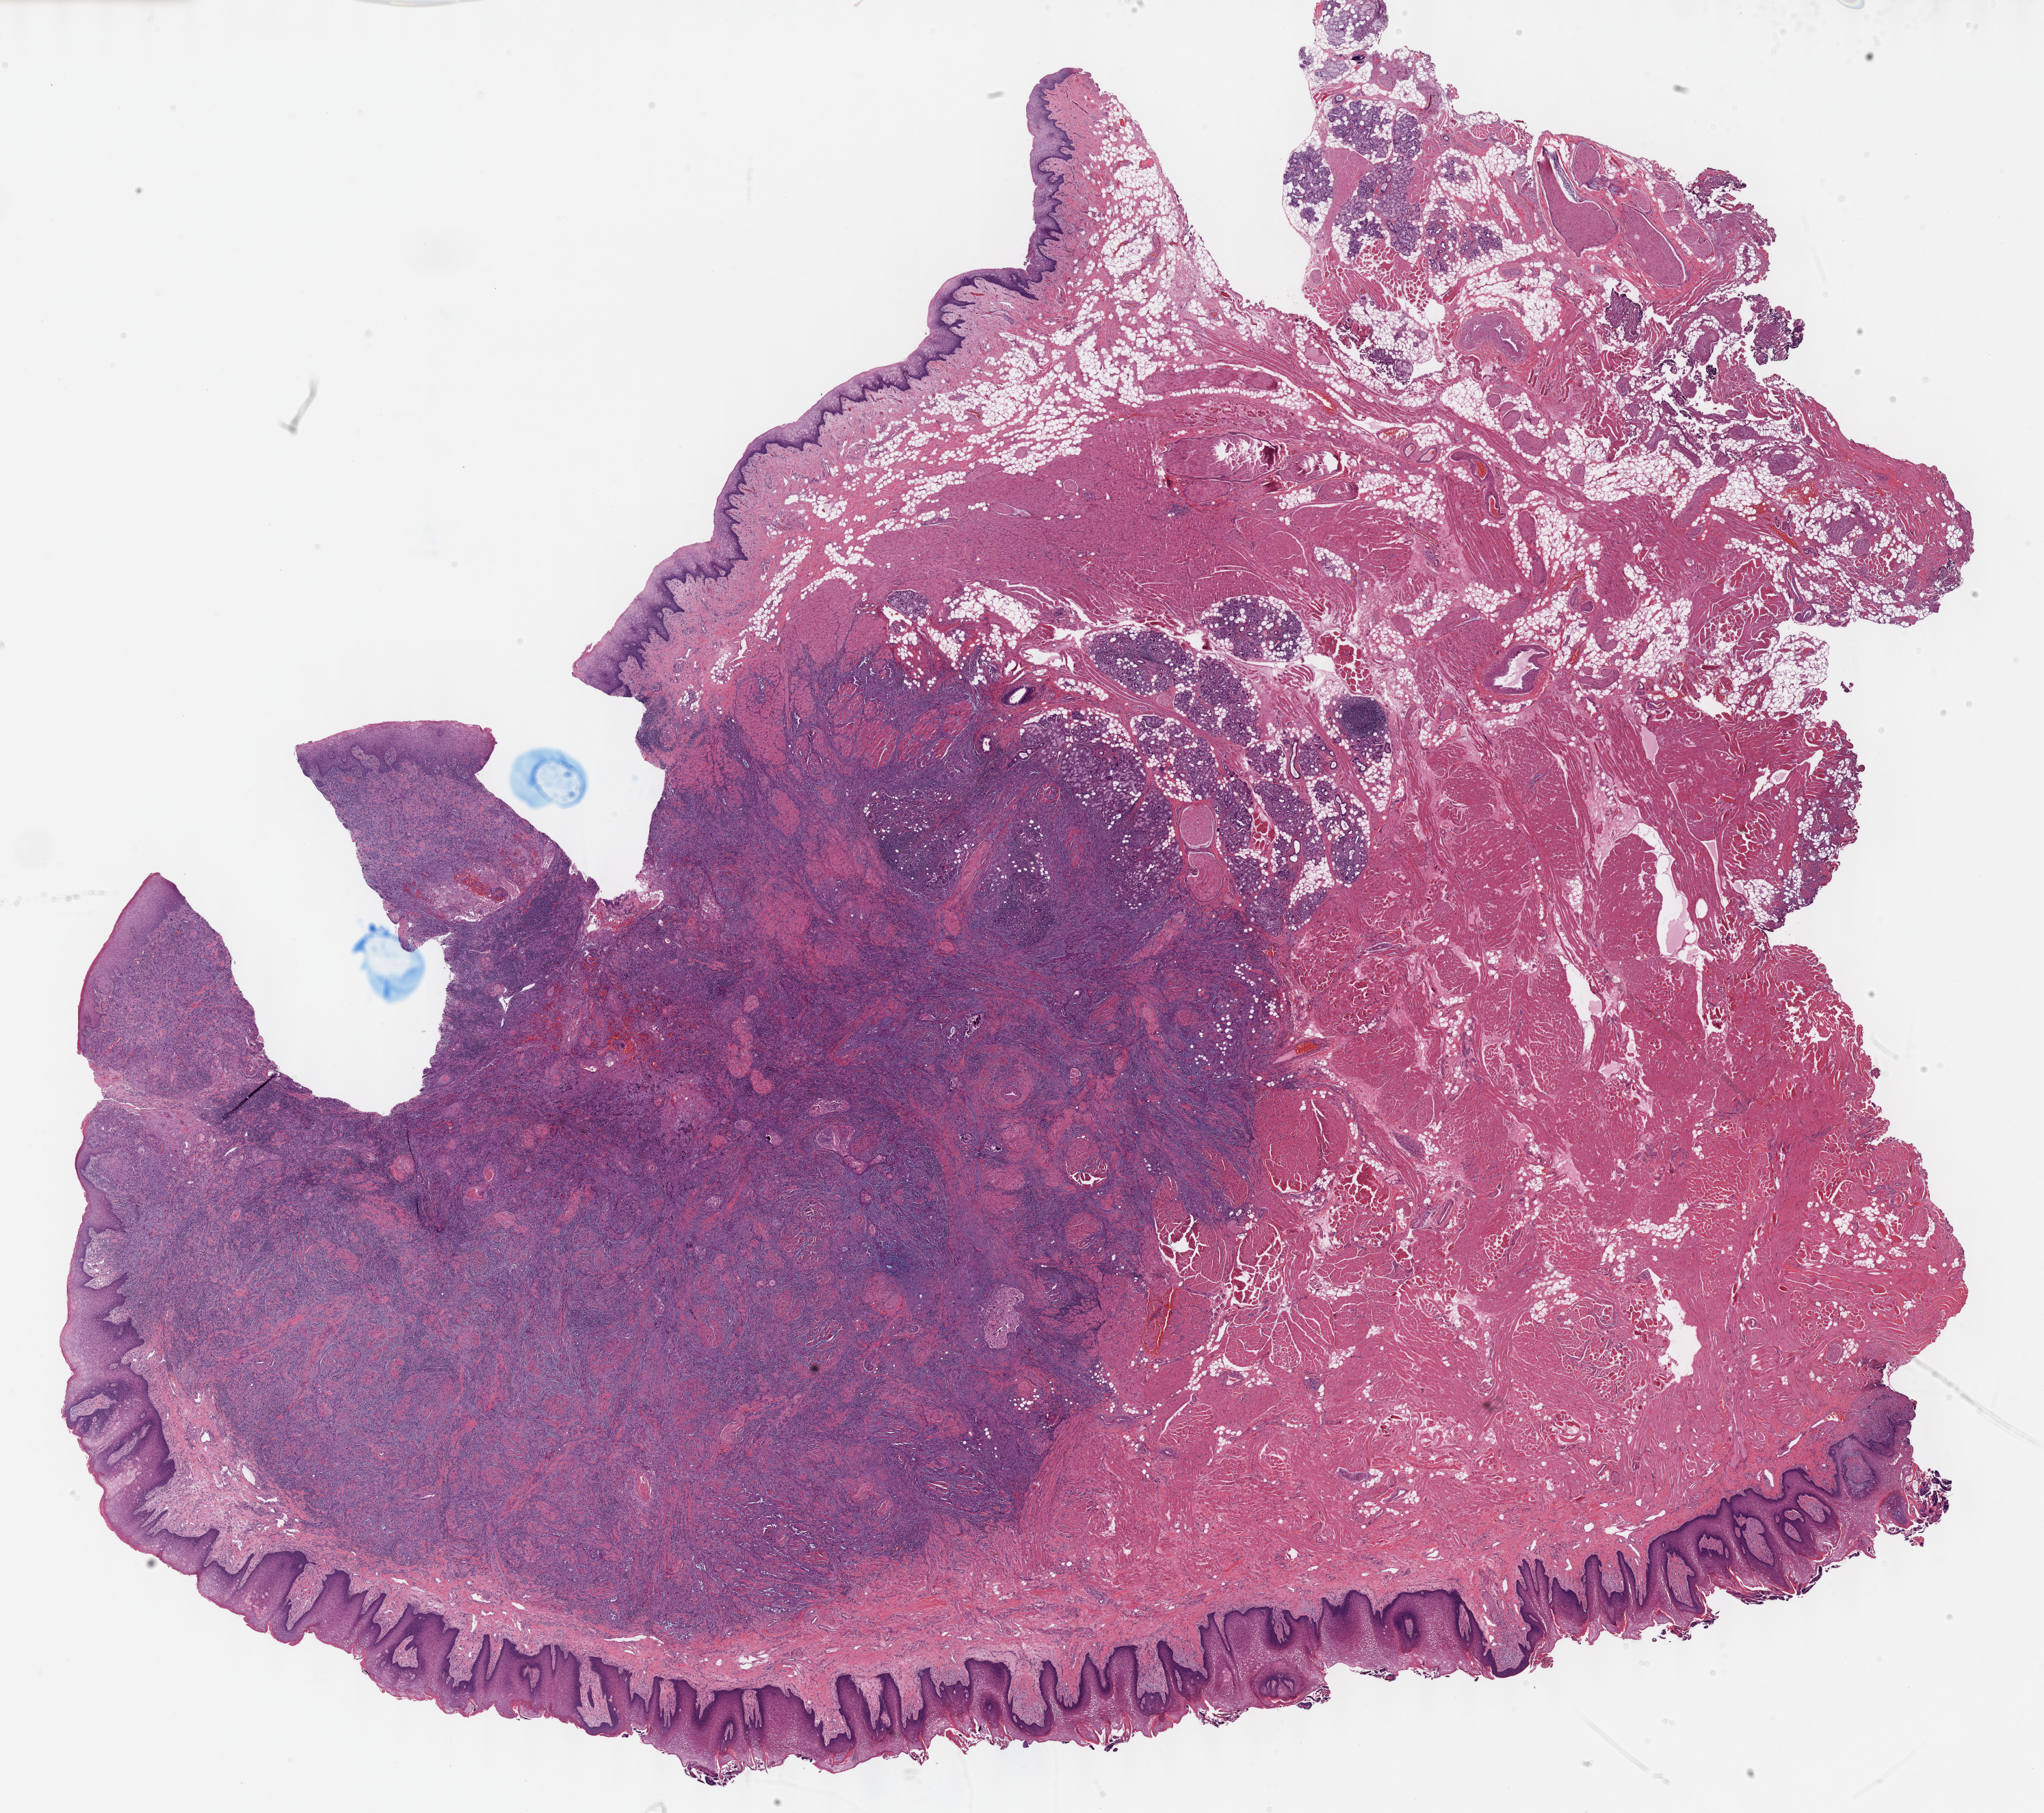
H&E whole-slide image — low-resolution overview of the scanned area, about 24.1 x 21.4 mm (acquisition: 40x scan). Formalin-fixed paraffin-embedded (FFPE) diagnostic section. Sample: primary tumour, head and neck. Male patient; age at initial diagnosis 58 years.
Diagnosis: Squamous cell carcinoma, NOS.